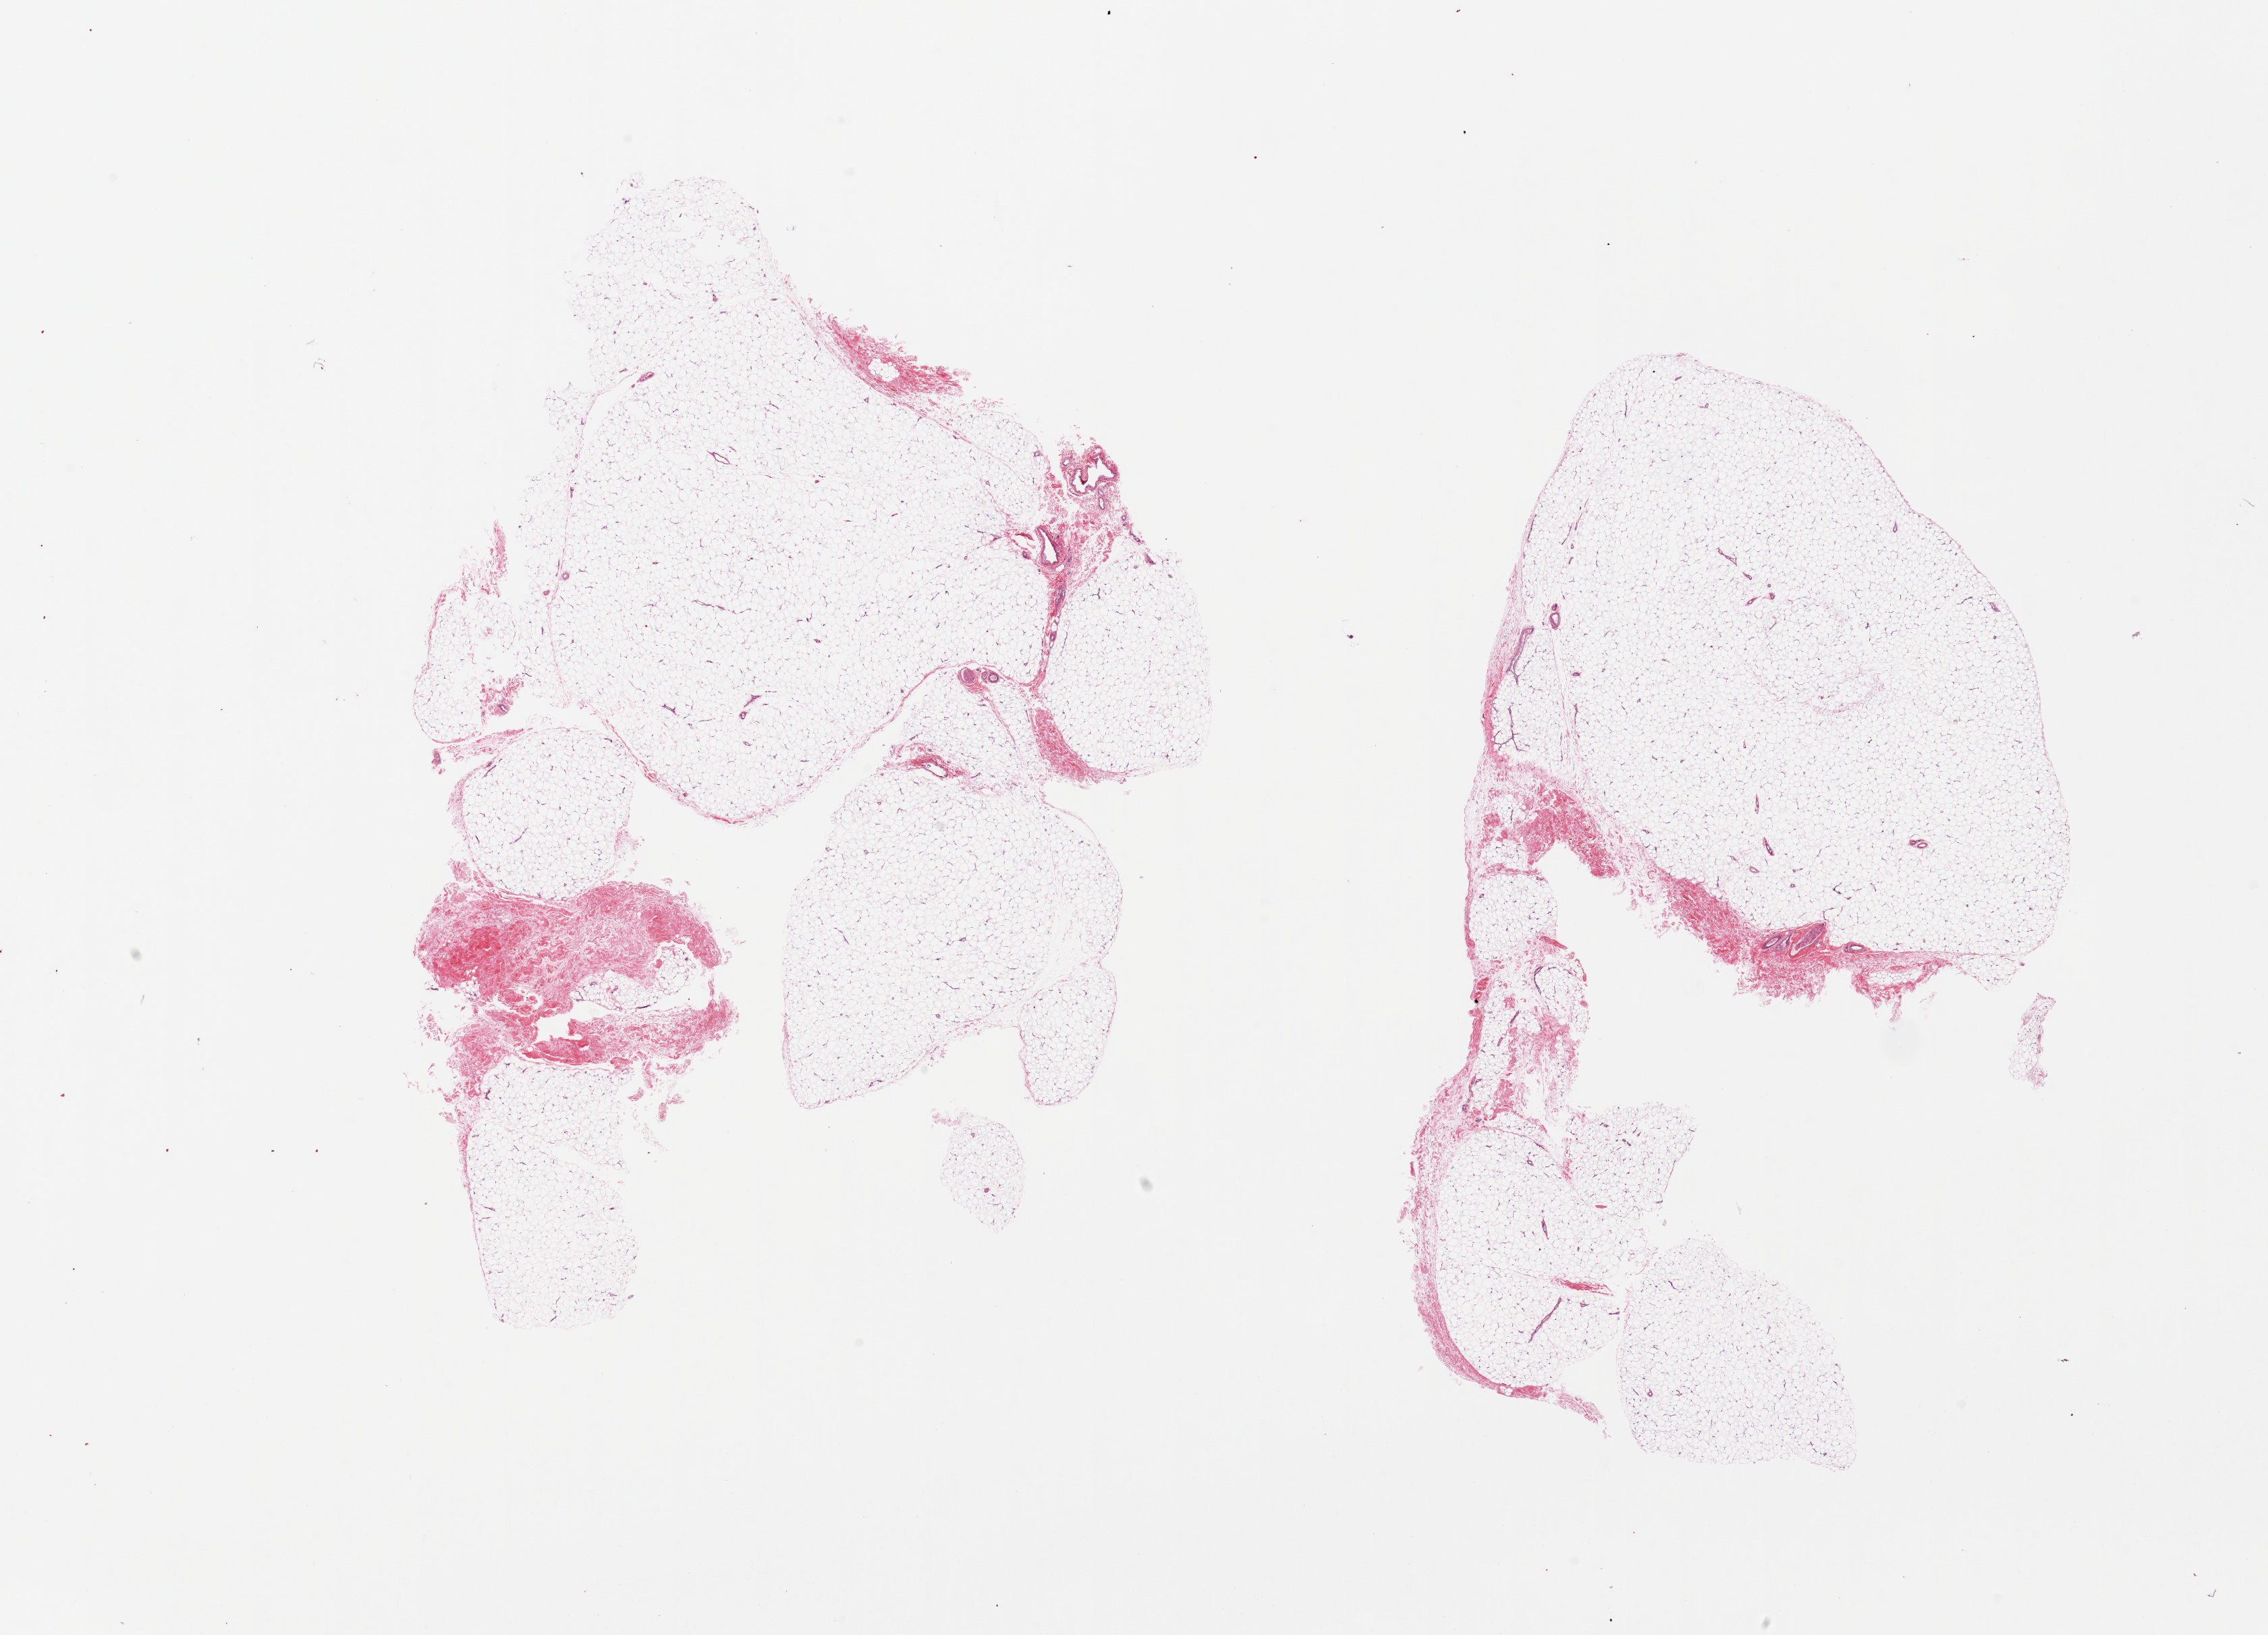
Digitized H&E-stained section, whole scanned area (about 26.6 x 19.2 mm) shown as a low-resolution overview; PAXgene-fixed, paraffin-embedded tissue; target tissue: adipose tissue; donor tissue sample. Donor: female.
Pathologist's review note for this sample: 2 pieces, internal holes.